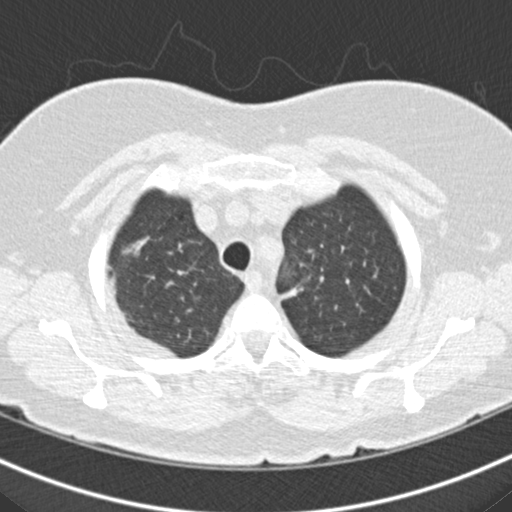
Low-dose screening chest CT, one axial slice. Slice 141 of 160 in the series (ordered by position). Reconstruction kernel B30f. 120 kVp. Lung window (W 1500 / L -600 HU). 512 × 512 image matrix, field of view 316 × 316 mm.
Annotated regions visible in this slice (outlined manually by an expert reader):
- lesion 3 (nodule, upper lobe of right lung): bounding box <131,236,149,252> (left, top, right, bottom; pixels)